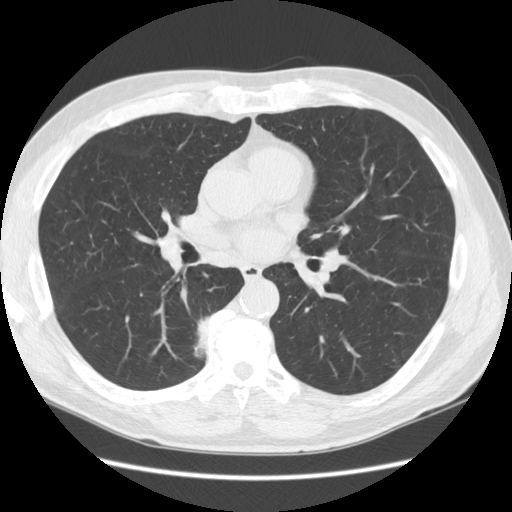
Low-dose screening chest CT, one axial slice; position 69 of 133 along the scan axis; reconstruction kernel STANDARD; 120 kVp; lung window (W 1500 / L -600 HU); 512 × 512 image matrix.
Structures marked on this image (expert manual segmentation):
- lesion 1 (tumor, lower lobe of right lung): bounding box (x1, y1, x2, y2) in pixels: (195, 317, 210, 358)